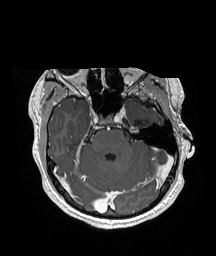
Brain MRI from a brain-tumour surgery series, one axial slice; position 123 of 192 along the scan axis; T1-weighted post-contrast; 216 × 256 image matrix. Case-level facts recorded for this patient, not image findings: histopathology: Glioneuronal tumor; WHO grade: 2; tumour location: Left Superior Temporal Gyrus.
Structures marked on this image (manually delineated by an expert):
- previous resection cavity: bounding box (x1, y1, x2, y2) in pixels: (135, 121, 148, 126)